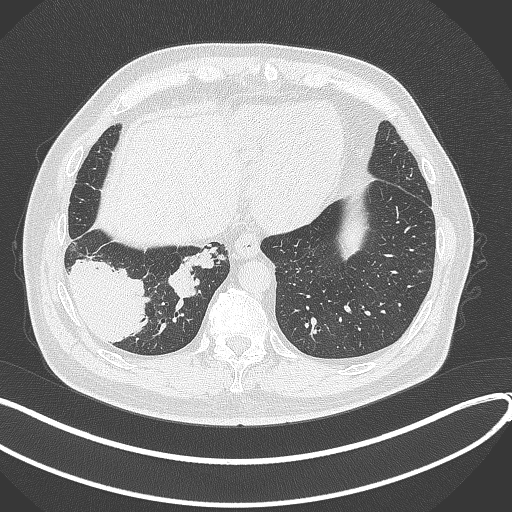
Chest CT, one axial slice; position 80 of 360 along the scan axis; reconstruction kernel B70f; 120 kVp; lung window (W 1500 / L -600 HU); 512 × 512 image matrix, field of view 400 × 400 mm. Patient: male, 59 years.
Annotated regions visible in this slice (bounding box drawn by a radiologist):
- lung tumour (recorded histology: adenocarcinoma): bounding box <64,254,151,349> (left, top, right, bottom; pixels)